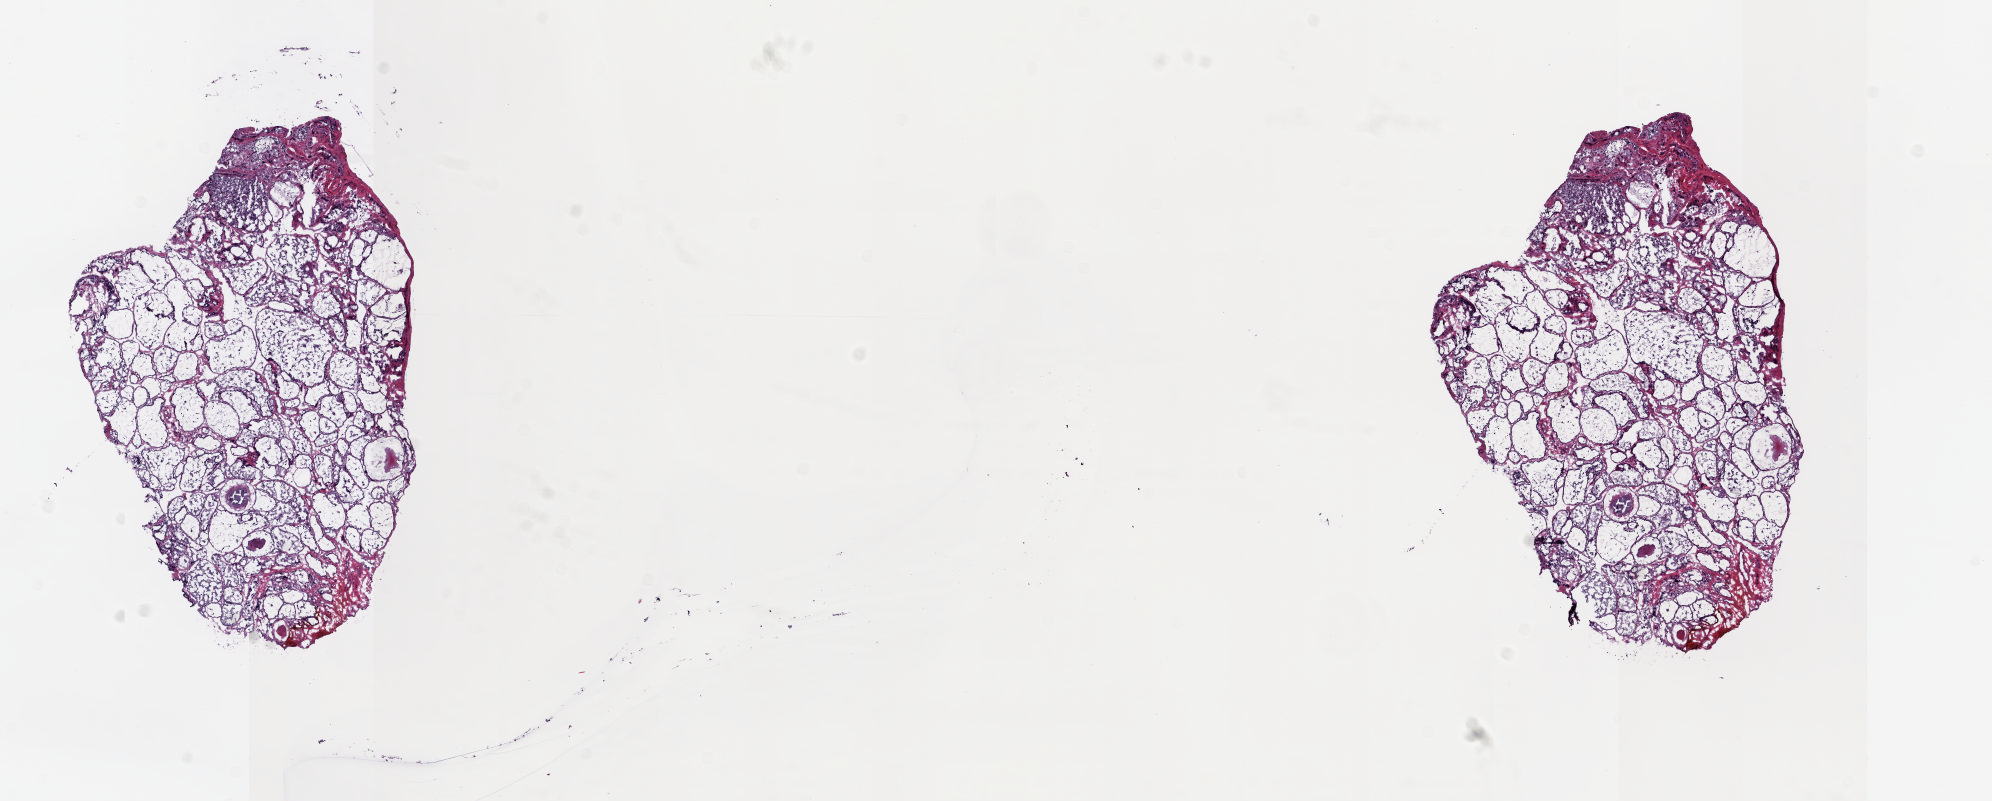
Digitized Hematoxylin and eosin (H&E) stained tissue section (whole slide), shown as a low-resolution overview of the whole scanned area (about 15.8 x 6.4 mm, slide scanned at 20x); frozen section from the top of the tissue portion; sample: solid tissue normal (non-tumour tissue), thyroid. Female patient; age at initial diagnosis 53 years. Pathologist review of this section (percent, as recorded): tumour cells 0%, tumour nuclei 0%.
This section: solid tissue normal sample (biorepository sample class). Patient diagnosis: Papillary carcinoma, follicular variant (thyroid gland).